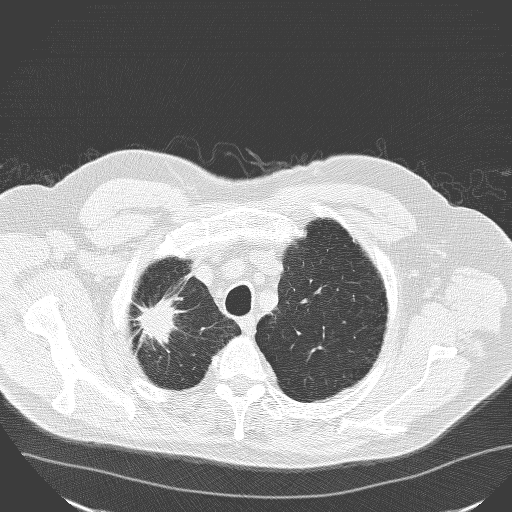
Low-dose screening chest CT, one axial slice. Position 139 of 160 along the scan axis. 120 kVp. Lung window (W 1500 / L -600 HU). 3.2 mm slice thickness. 512 × 512 image matrix, field of view 400 × 400 mm.
Outlined on this slice (outlined manually by an expert reader):
- lesion 1 (tumor, upper lobe of right lung): box from (x=136, y=299) to (x=176, y=340) px